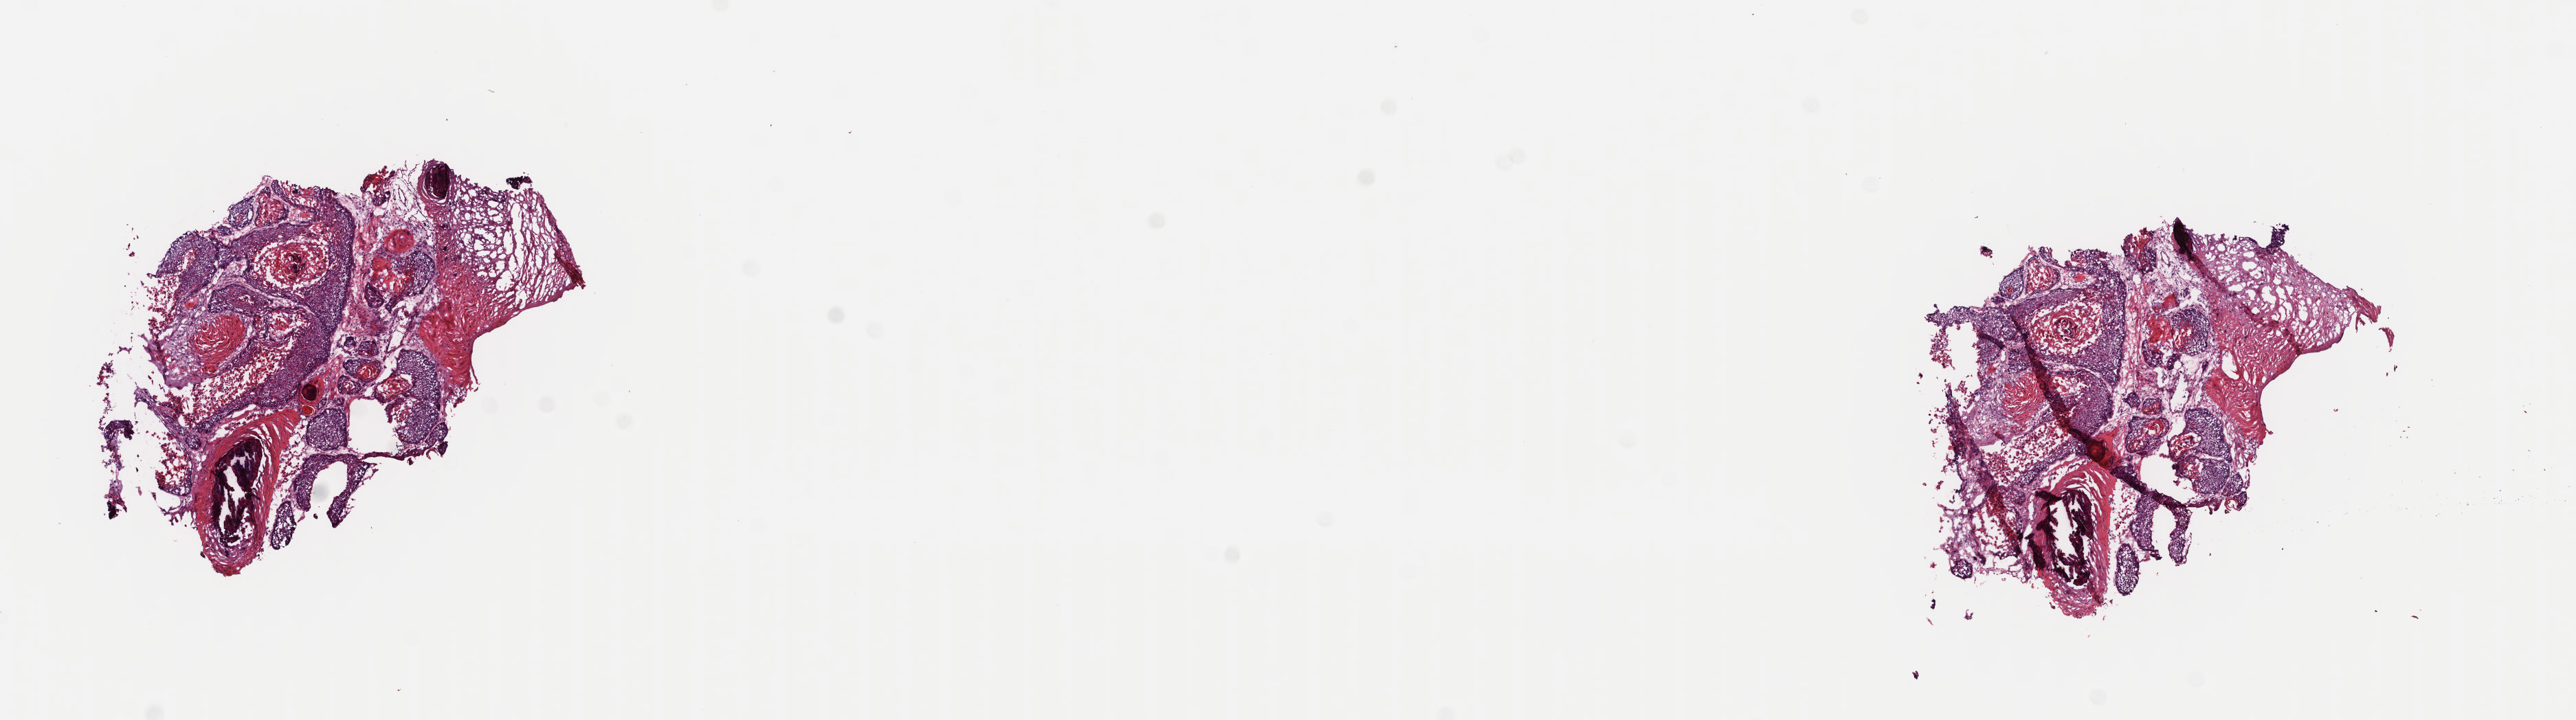
Whole-slide histology image, Hematoxylin and eosin (H&E) stained, whole scanned area (about 14.8 x 4.1 mm) shown as a low-resolution overview, frozen section from the top of the tissue portion, sample: primary tumour, head and neck. Male, age 63 years at initial diagnosis. Histologic grade: G3 (poorly differentiated). Pathologist review of this section (percent, as recorded): tumour cells 100%, tumour nuclei 75%, normal cells 0%, stromal cells 0%, necrosis 0%. Infiltration values recorded for this section: lymphocyte infiltration 4%, monocyte infiltration 0%, neutrophil infiltration 0%.
AJCC pathologic stage: IVA (7th edition). Diagnosis: Squamous cell carcinoma, NOS.